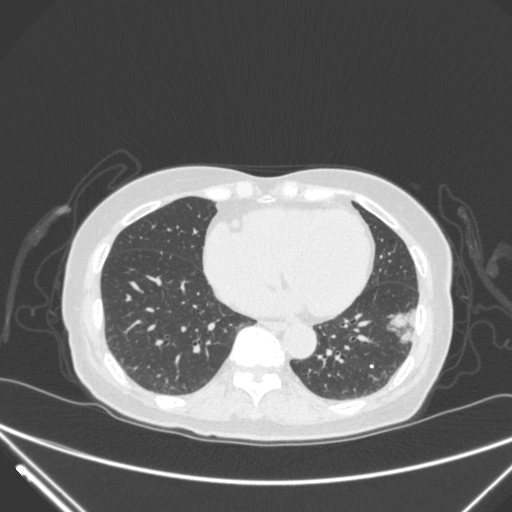
Chest CT, one axial slice; slice 109 of 310 in the series (ordered by position); 120 kVp; lung window (W 1500 / L -600 HU); 1 mm slice thickness; 512 × 512 image matrix. Female patient, age 82 years. Case-level facts recorded for this patient, not image findings: clinical TNM (as recorded): T1c N0 M0.
Structures marked on this image (bounding box drawn by a radiologist):
- lung tumour (recorded histology: adenocarcinoma): bounding box <380,298,428,359> (left, top, right, bottom; pixels)